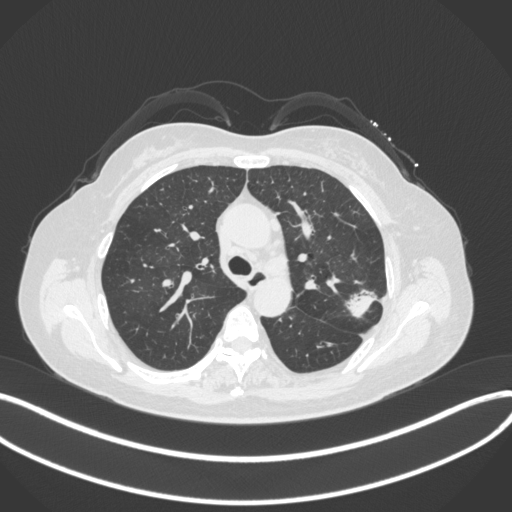
Chest CT, one axial slice; slice 233 of 330 in the series (ordered by position); reconstruction kernel B31f; lung window (W 1500 / L -600 HU); 512 × 512 image matrix, field of view 400 × 400 mm. Female patient, age 60 years. From the clinical record (not read from this slice): clinical TNM (as recorded): T1c N0 M0.
Annotated regions visible in this slice (bounding box drawn by a radiologist):
- lung tumour (recorded histology: adenocarcinoma): box from (x=340, y=282) to (x=378, y=321) px